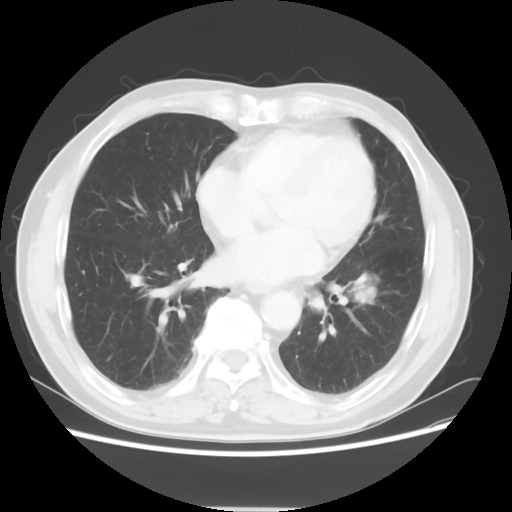
Chest CT, one axial slice. Reconstruction kernel STANDARD. 120 kVp. Lung window (W 1500 / L -600 HU). 5 mm slice thickness. 512 × 512 image matrix, field of view 366 × 366 mm. Patient: male, 71 years. Case-level facts recorded for this patient, not image findings: clinical TNM (as recorded): T1c N1 M0; histopathological grade: G2-3.
Structures marked on this image (rectangle marked by the reading radiologist):
- lung tumour (recorded histology: adenocarcinoma): bounding box <344,267,384,316> (left, top, right, bottom; pixels)